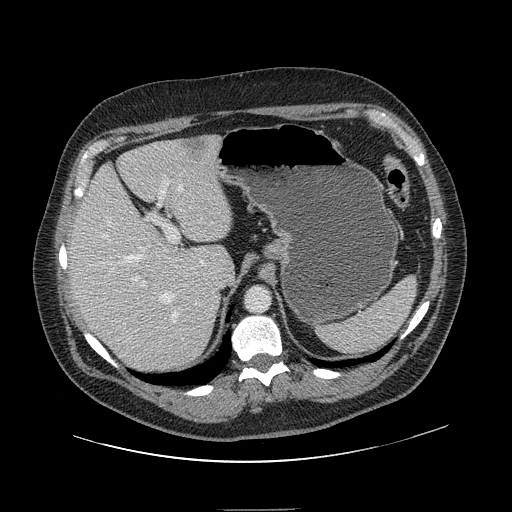
Contrast-enhanced abdominal CT, one axial slice. Slice 105 of 154 in the series (ordered by position). 120 kVp. Intravenous contrast given. Soft-tissue window (W 400 / L 40 HU). 512 × 512 image matrix. Male patient, age 61 years. From the clinical record (not read from this slice): diagnosis: colorectal cancer liver metastases, imaged before liver resection; multiple liver metastases: yes; largest metastasis: 2.6 cm.
Structures marked on this image (manually delineated by an expert):
- hepatic veins: bounding box <101,184,183,323> (left, top, right, bottom; pixels)
- liver: <68,137,232,374>
- planned liver remnant (the part of the liver to remain after resection): <68,144,232,360>
- portal vein (with intrahepatic branches): <133,176,184,286>
- liver metastasis: <183,139,207,163>